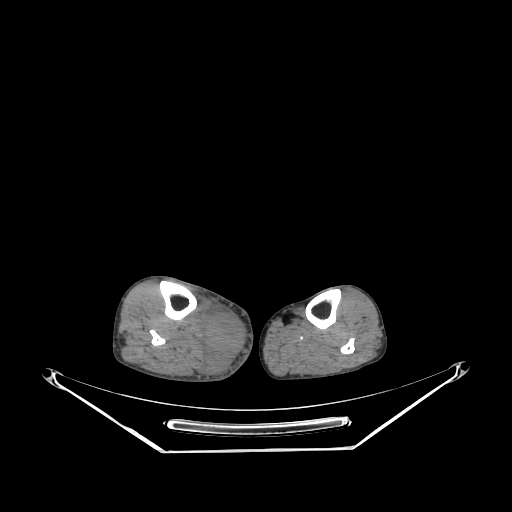
CT of an extremity soft-tissue mass (from a PET/CT study), one axial slice; reconstruction kernel SOFT; 140 kVp; soft-tissue window (W 400 / L 40 HU); 3.75 mm slice thickness; 512 × 512 image matrix, field of view 500 × 500 mm. Male patient. Case-level facts recorded for this patient, not image findings: histological type: pleiomorphic liposarcoma; grade: high; site of the primary tumour: right calf.
Structures marked on this image (expert contour drawn on MRI and transferred to this co-registered scan by the dataset authors):
- gross tumour volume including surrounding oedema: box from (x=201, y=304) to (x=248, y=376) px
- gross tumour volume (mass): (x=203, y=310)–(x=248, y=353)